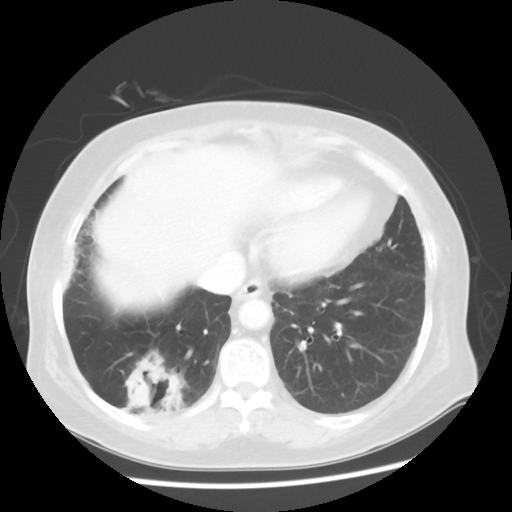
Chest CT, one axial slice. Slice 17 of 56 in the series (ordered by position). Reconstruction kernel STANDARD. 120 kVp. Lung window (W 1500 / L -600 HU). 5 mm slice thickness. 512 × 512 image matrix. Female patient, age 64 years. Case-level facts recorded for this patient, not image findings: clinical TNM (as recorded): Tis N0 M0.
Annotated regions visible in this slice (bounding box drawn by a radiologist):
- lung tumour (recorded histology: adenocarcinoma): bounding box [x1, y1, x2, y2] px = [114, 339, 197, 428]